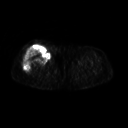
FDG PET of an extremity soft-tissue mass (from a PET/CT study), one axial slice; 3.27 mm slice thickness; 128 × 128 image matrix. Patient: female, 57 years. From the clinical record (not read from this slice): histological type: pleiomorphic undifferentiated sarcoma; grade: high; site of the primary tumour: right quadricep.
Annotated regions visible in this slice (expert contour drawn on MRI and transferred to this co-registered scan by the dataset authors):
- tumour plus oedema (research contour): bounding box (x1, y1, x2, y2) in pixels: (23, 46, 49, 72)
- tumour (research contour): (23, 46, 49, 72)